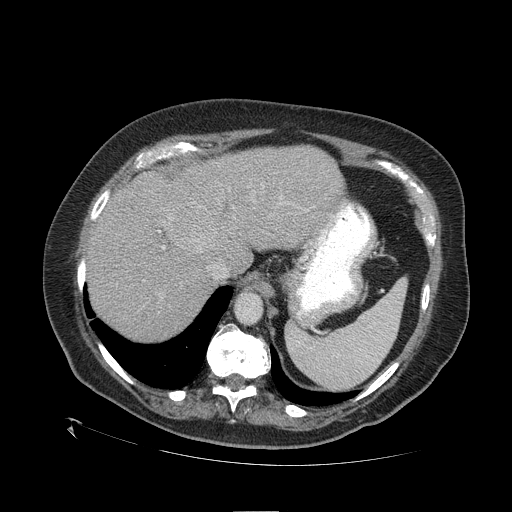
Contrast-enhanced abdominal CT (liver protocol), one axial slice. Position 82 of 109 along the scan axis. Reconstruction kernel STANDARD. 120 kVp. One of 2 acquisitions stored at this slice position. Soft-tissue window (W 400 / L 40 HU). 512 × 512 image matrix, field of view 460 × 460 mm. Case-level facts recorded for this patient, not image findings: diagnosis: hepatocellular carcinoma (patient treated with transarterial chemoembolisation; whether this scan precedes or follows treatment is not stated here); TNM stage (as recorded): Stage-I; Child-Pugh class: A; tumour differentiation: no biopsy; tumour size: 4.6 cm.
Structures marked on this image (semi-automatic segmentation, software-assisted and operator-edited):
- liver parenchyma outside the tumour (the mass and vessels are separate outlines, so this box may not span the whole liver): bounding box (x1, y1, x2, y2) in pixels: (88, 146, 344, 340)
- mass: (160, 199, 222, 254)
- liver vessels: (158, 196, 289, 249)